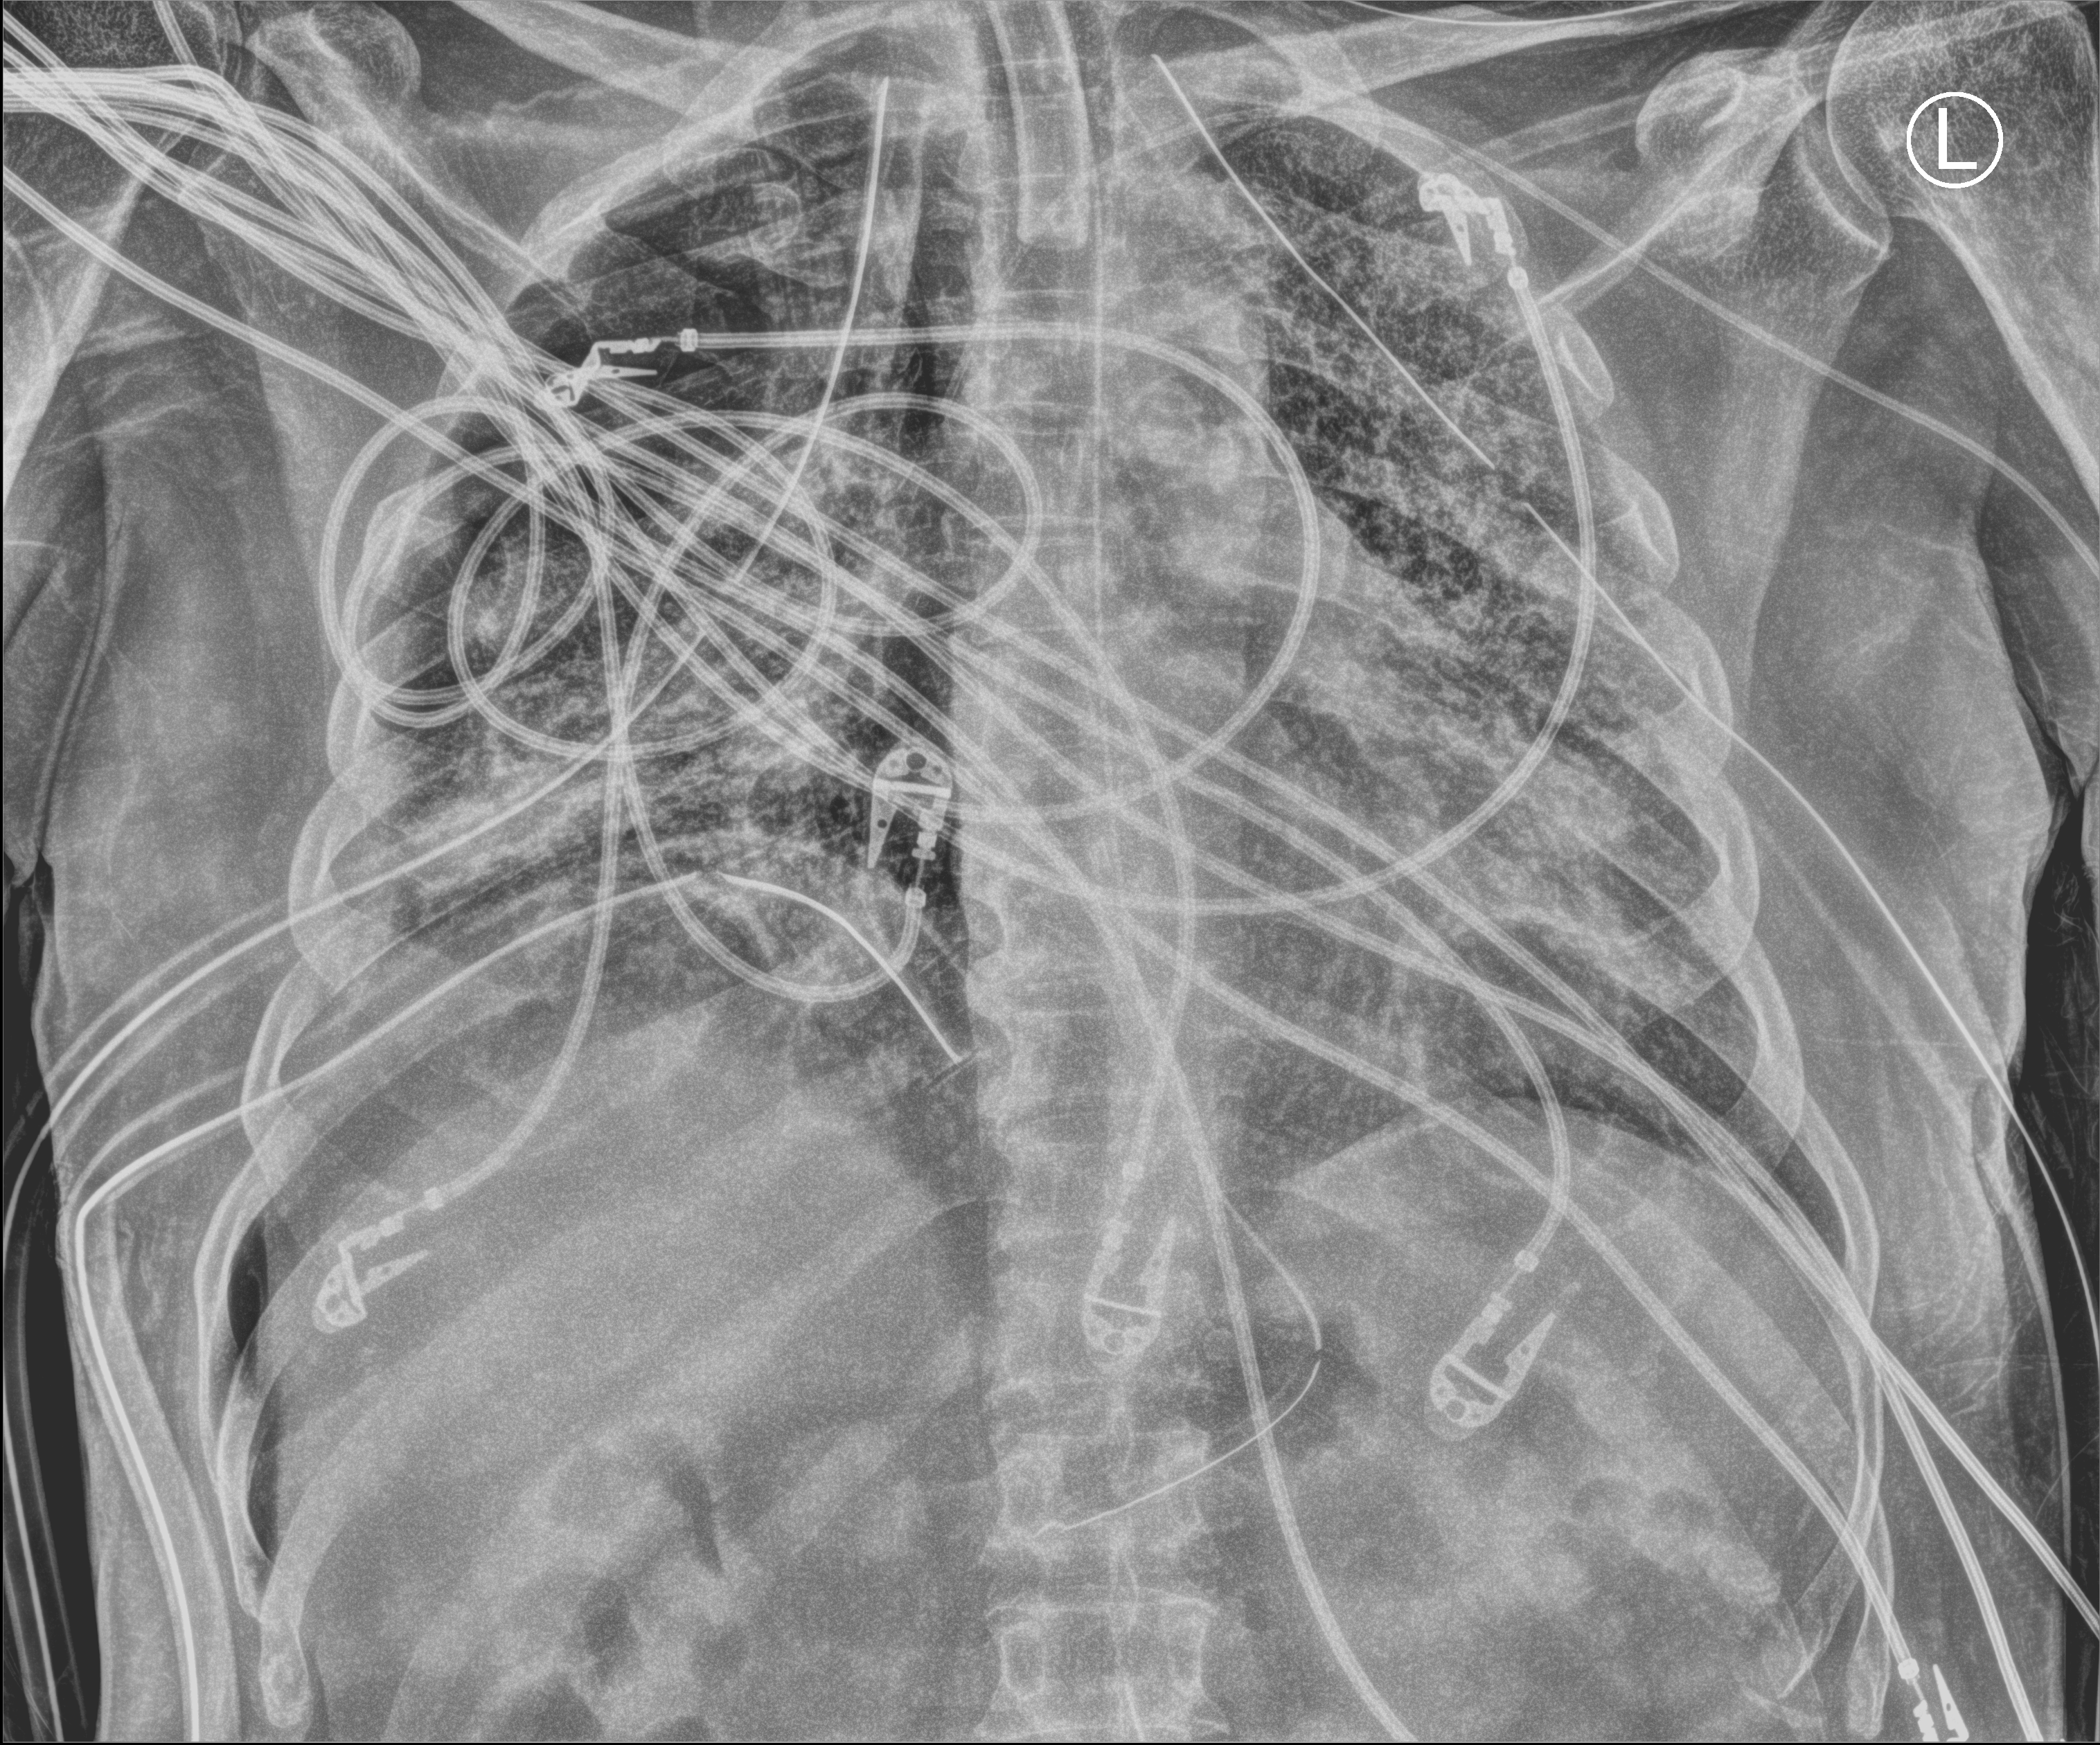
Chest X-ray (portable), anteroposterior (AP) projection. Male patient hospitalised with COVID-19, age 18–59 years.
Admission-level facts for this patient (not findings on this image; timing relative to this image not recorded):
- COPD (admission record): no
- mechanically ventilated during this hospital stay: yes
- admitted to intensive care during this hospital stay: yes